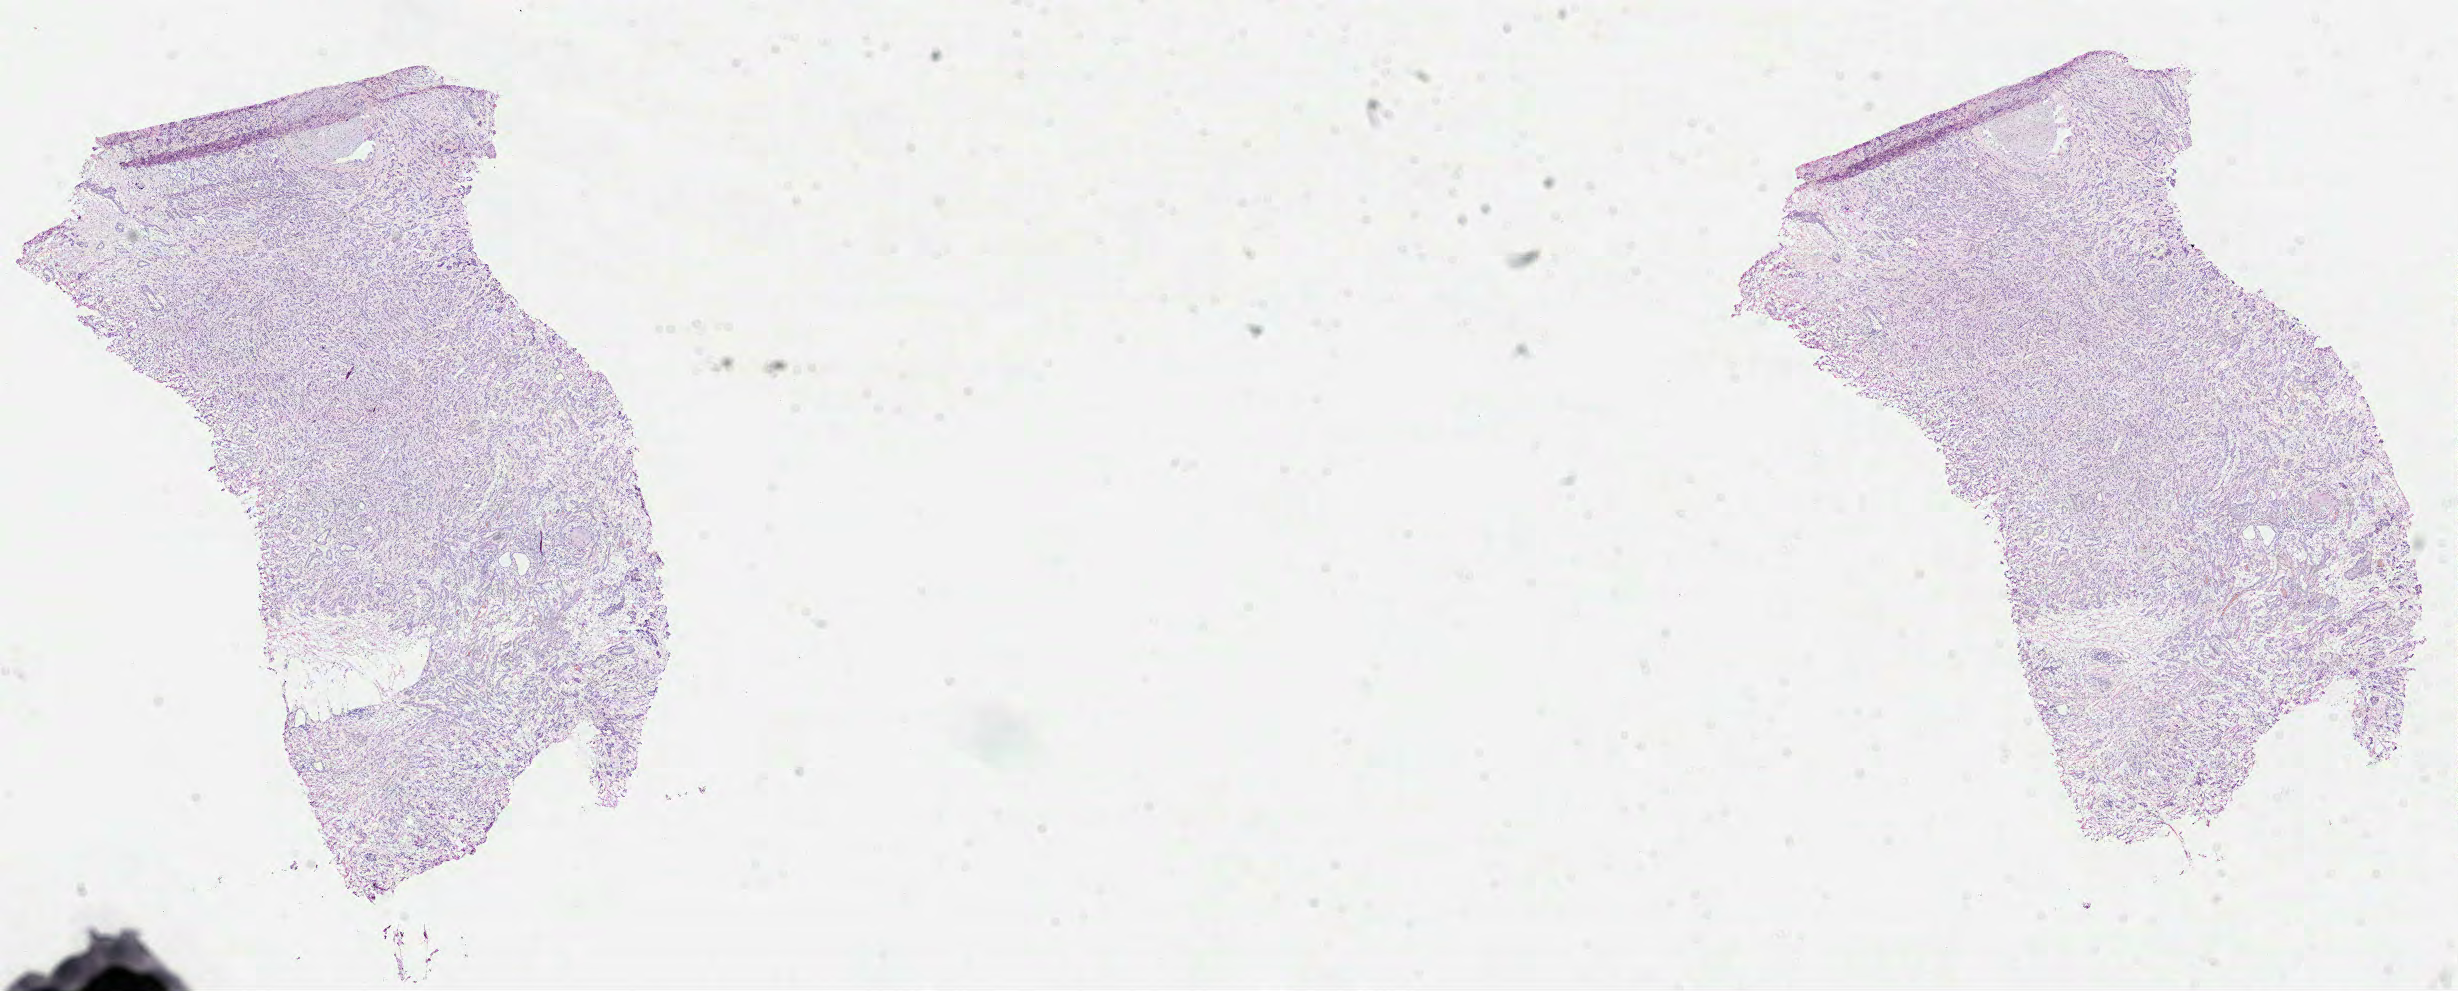
Whole-slide histology image, Hematoxylin and eosin (H&E) stained — shown as a low-resolution overview of the whole scanned area (about 19.8 x 8.0 mm, acquisition: 40x scan); formalin-fixed paraffin-embedded (FFPE) diagnostic section; primary tumour sample from the prostate. Male, age 68 years at initial diagnosis. Gleason score: 7 (3+4).
• diagnosis: Acinar cell carcinoma (prostate gland)